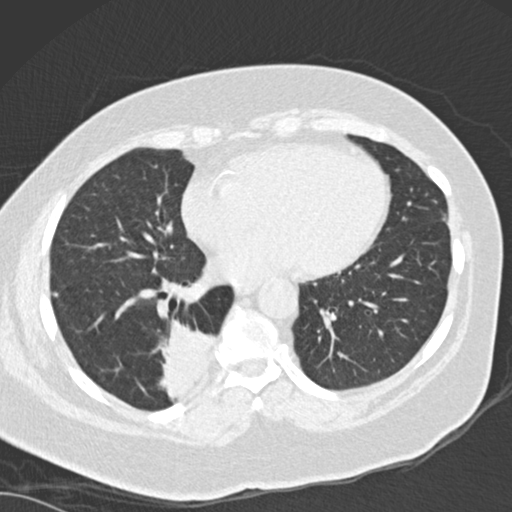
Chest CT (low-dose screening protocol), one axial image; first (baseline) screen; lung window (W 1500 / L -600 HU); 2 mm slice thickness. Female participant, aged 66 years at enrolment. Current smoker at enrolment.
Lesion marked by an expert reader, bounding box <148,318,230,402> (left, top, right, bottom; pixels). The screening reader recorded 3 non-calcified nodules or masses ≥4 mm on this exam (left lower lobe, left lower lobe, right lower lobe); which of them this box marks is not recorded. Official screen result: positive, change unspecified: nodule(s) >= 4 mm or enlarging nodule(s), mass(es), or other non-specific abnormalities suspicious for lung cancer. Participant outcome: lung cancer diagnosed 67 days after this screen — adenocarcinoma, NOS, right lower lobe, well differentiated (G1), stage IB (AJCC 6th edition), 55 mm at pathology.